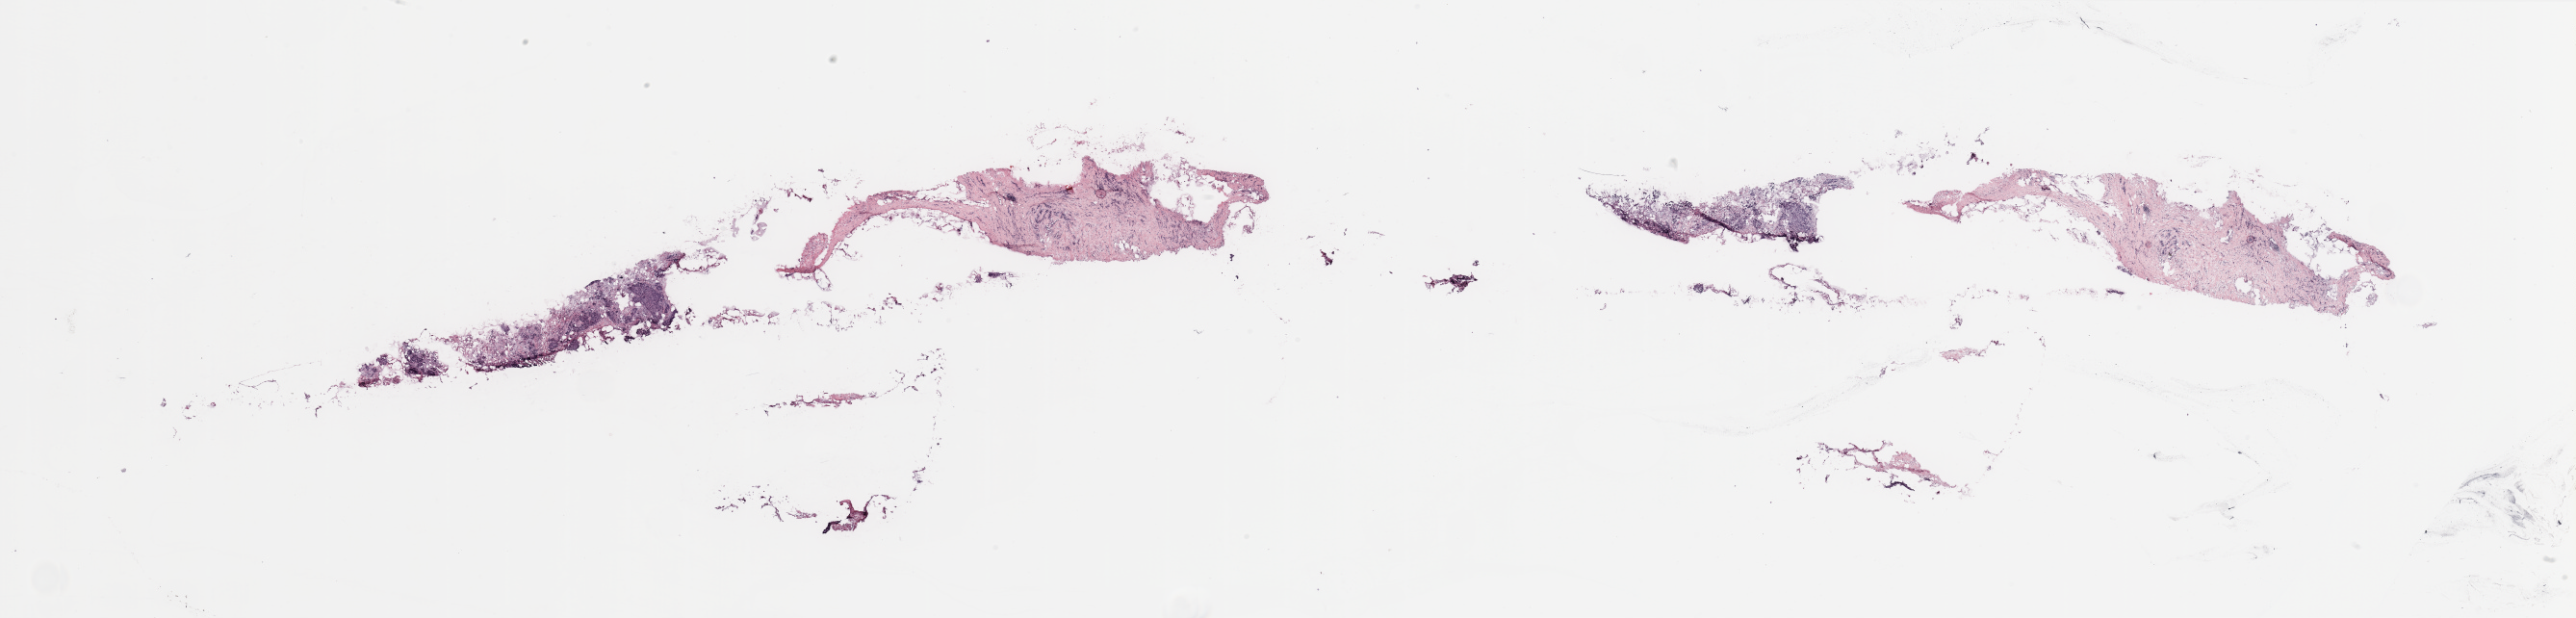
Digitized Hematoxylin and eosin (H&E) stained tissue section (whole slide), whole scanned area (about 42.3 x 10.2 mm) shown as a low-resolution overview, breast, tissue type not recorded.
Patient diagnosis (cohort enrolment): breast cancer (breast).